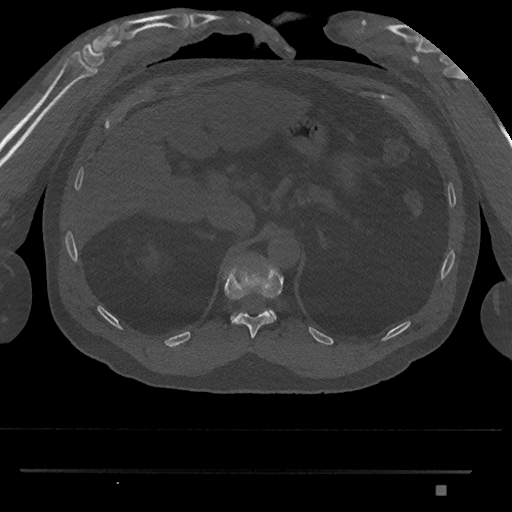
CT including the spine, one axial slice; bone window (W 1800 / L 400 HU); 512 × 512 image matrix. Male patient, age 65 years. From the clinical record (not read from this slice): primary cancer: prostate.
Annotated regions visible in this slice (semi-automatic segmentation, software-assisted and operator-edited):
- T11 vertebra: bounding box (x1, y1, x2, y2) in pixels: (222, 263, 284, 339)
- T12 vertebra: (230, 309, 277, 320)